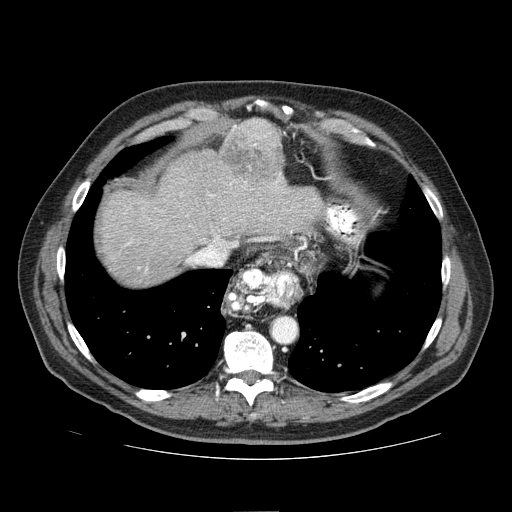
Contrast-enhanced abdominal CT (liver protocol), one axial slice; position 64 of 81 along the scan axis; 100 kVp; one of 2 acquisitions stored at this slice position; soft-tissue window (W 400 / L 40 HU); 2.5 mm slice thickness; 512 × 512 image matrix, field of view 400 × 400 mm. Case-level facts recorded for this patient, not image findings: diagnosis: hepatocellular carcinoma (patient treated with transarterial chemoembolisation; whether this scan precedes or follows treatment is not stated here); TNM stage (as recorded): Stage-IIIA; Child-Pugh class: A; tumour differentiation: well differentiated; tumour size: 5.6 cm.
Annotated regions visible in this slice (semi-automatically segmented with operator editing):
- abdominal aorta: box from (x=273, y=318) to (x=296, y=342) px
- liver parenchyma outside the tumour (the mass and vessels are separate outlines, so this box may not span the whole liver): (x=100, y=150)–(x=324, y=286)
- mass: (x=217, y=117)–(x=284, y=184)
- liver vessels: (x=126, y=177)–(x=280, y=271)